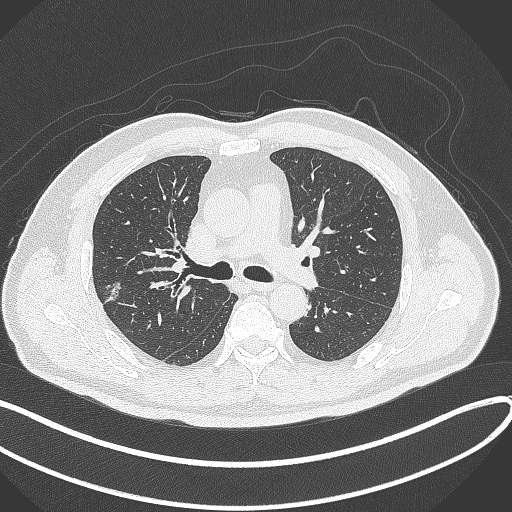
Chest CT, one axial slice. Position 211 of 372 along the scan axis. Lung window (W 1500 / L -600 HU). 512 × 512 image matrix, field of view 400 × 400 mm. Patient: male, 60 years. From the clinical record (not read from this slice): clinical TNM (as recorded): T1c N0 M0.
Annotated regions visible in this slice (rectangle marked by the reading radiologist):
- lung tumour (recorded histology: adenocarcinoma): box from (x=100, y=276) to (x=126, y=308) px